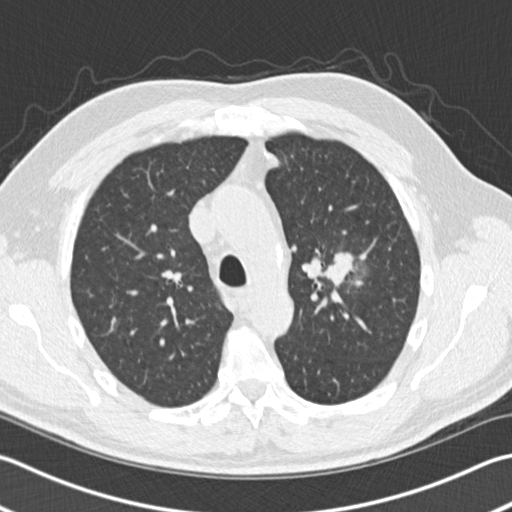
Low-dose screening chest CT, one axial slice. Position 109 of 153 along the scan axis. Reconstruction kernel B30f. Lung window (W 1500 / L -600 HU). 512 × 512 image matrix, field of view 346 × 346 mm.
Annotated regions visible in this slice (manually delineated by an expert):
- lesion 1 (tumor, upper lobe of left lung): box from (x=325, y=253) to (x=353, y=285) px